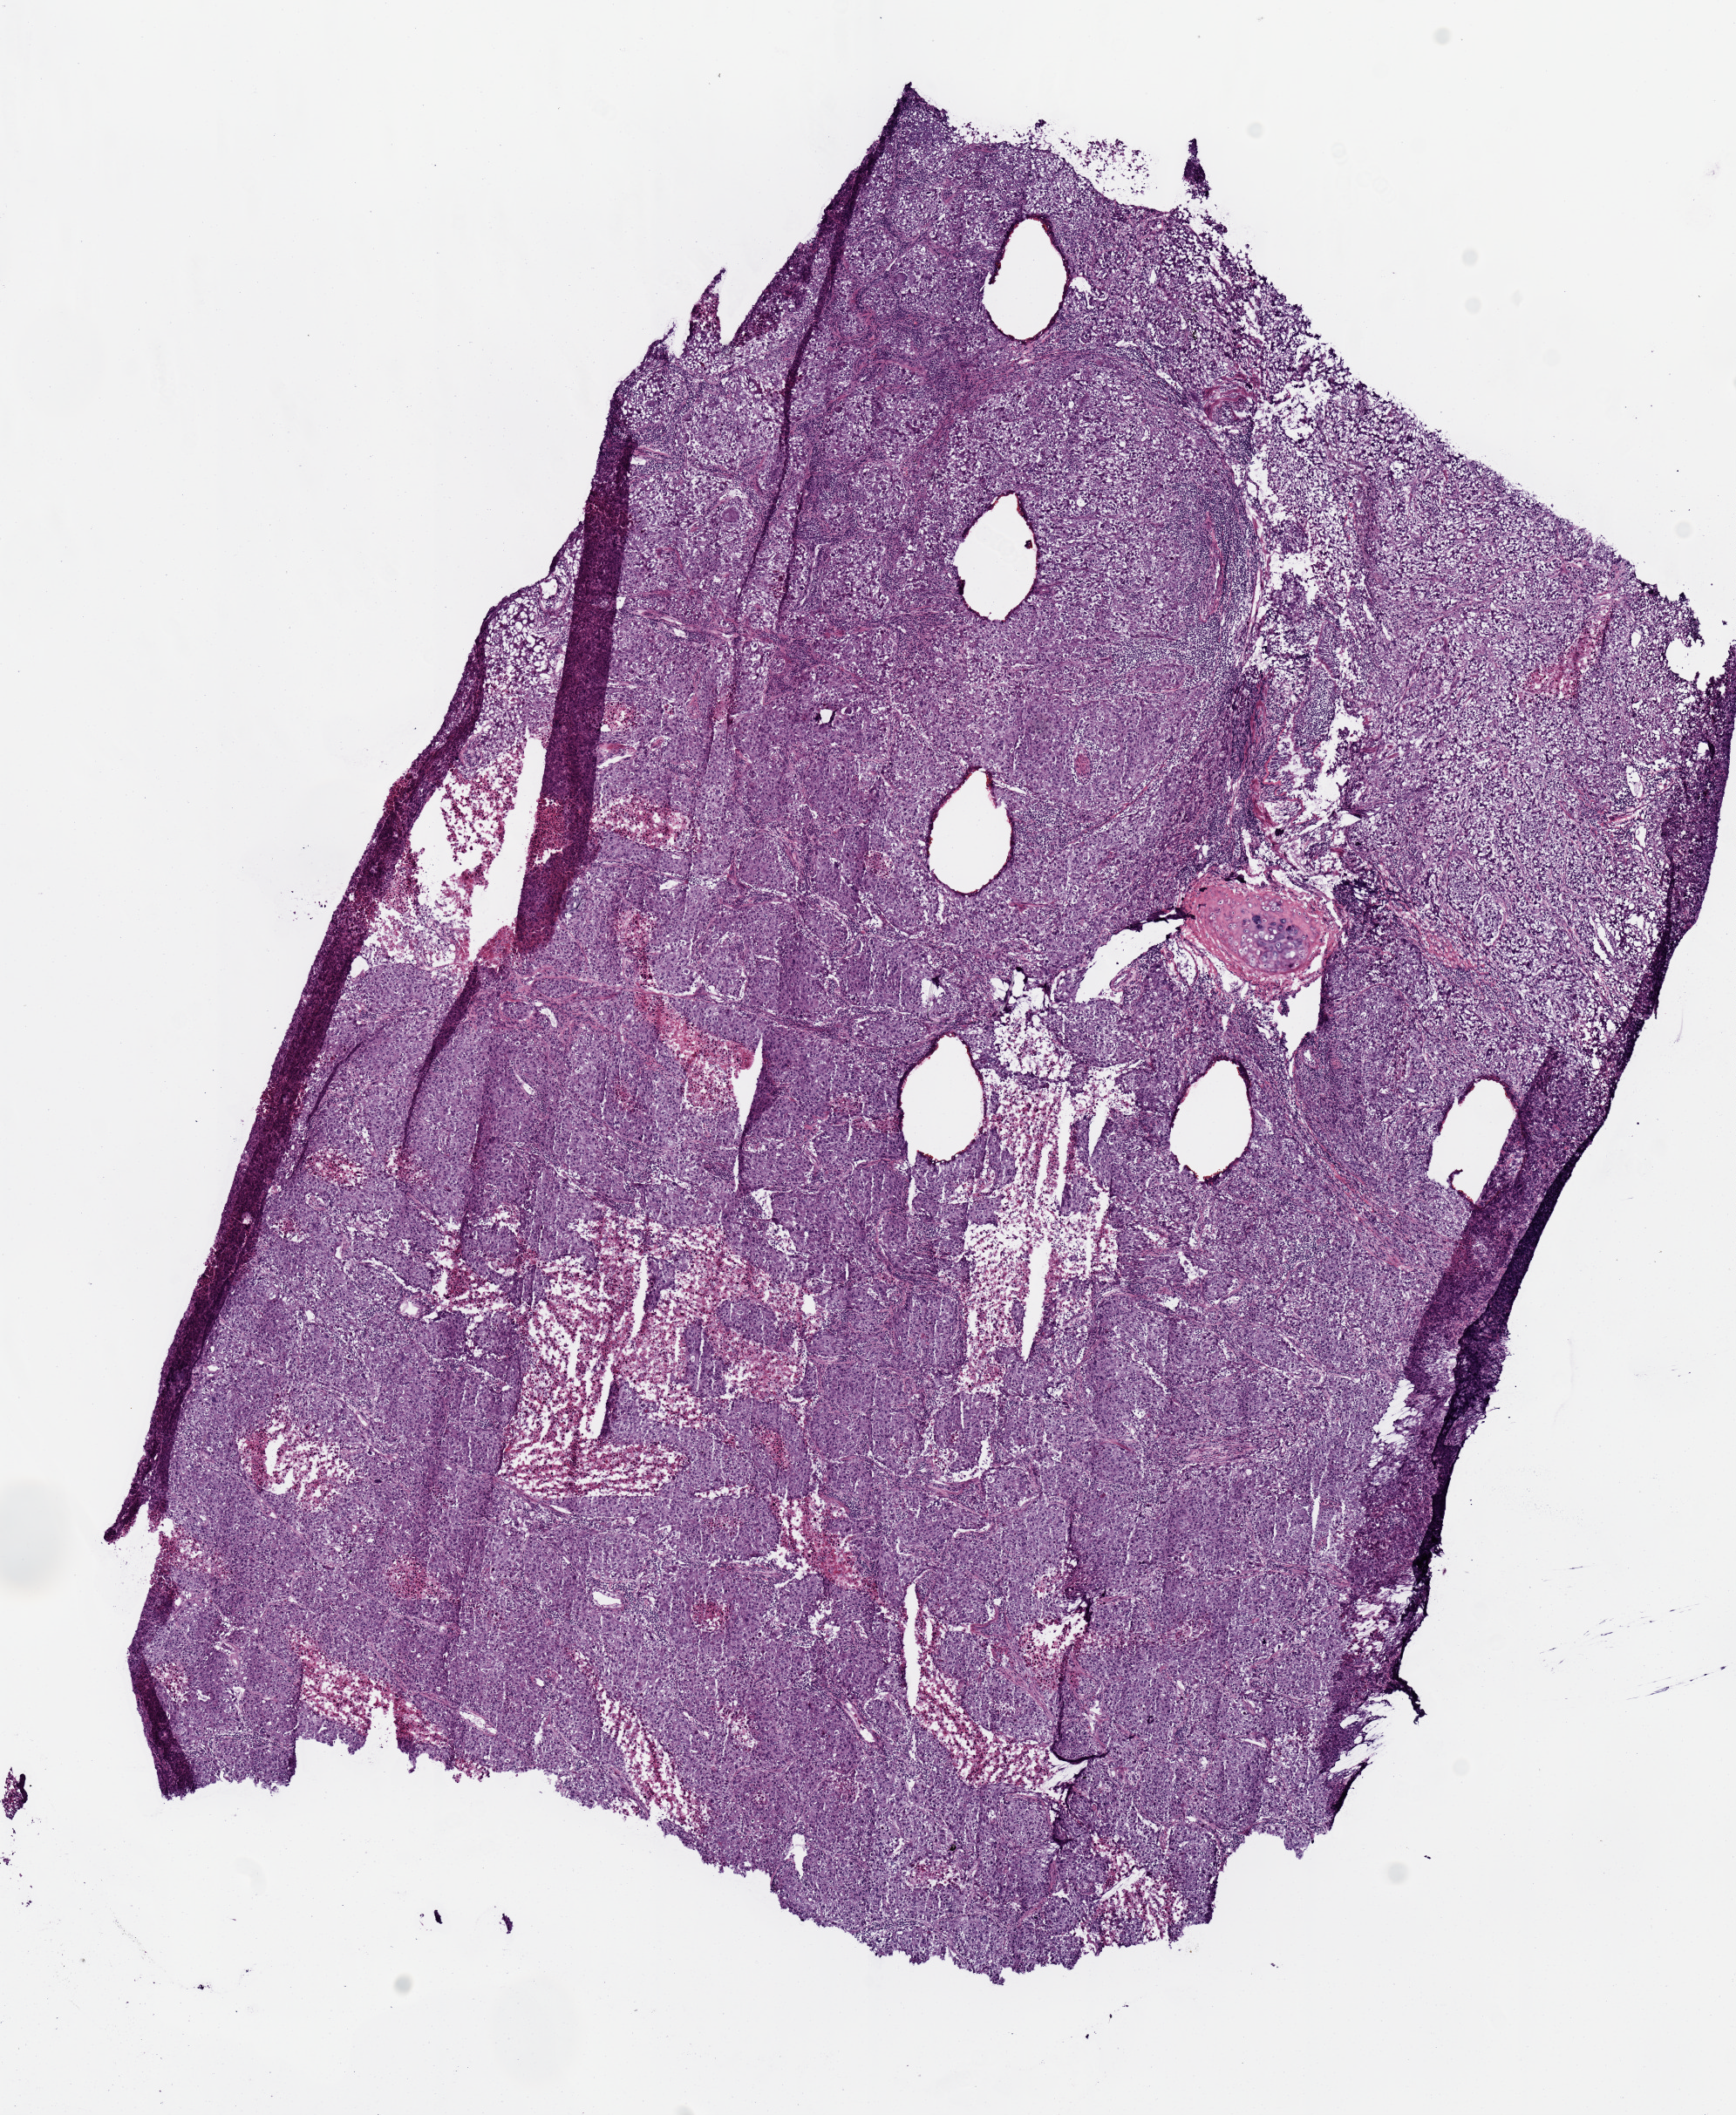
Digitized H&E-stained tissue section (whole slide) — shown as a low-resolution overview of the whole scanned area (about 7.9 x 9.6 mm, acquisition: 20x scan). Frozen section from the top of the tissue portion. Primary tumour sample from the lung. Patient: male, age at initial diagnosis 81 years. Composition of this section per pathologist review: tumour cells 85%, tumour nuclei 70%, normal cells 0%, stromal cells 5%, necrosis 10%.
* histologic diagnosis: Adenocarcinoma, NOS (upper lobe, lung)
* AJCC pathologic stage: IIB
* laterality: right